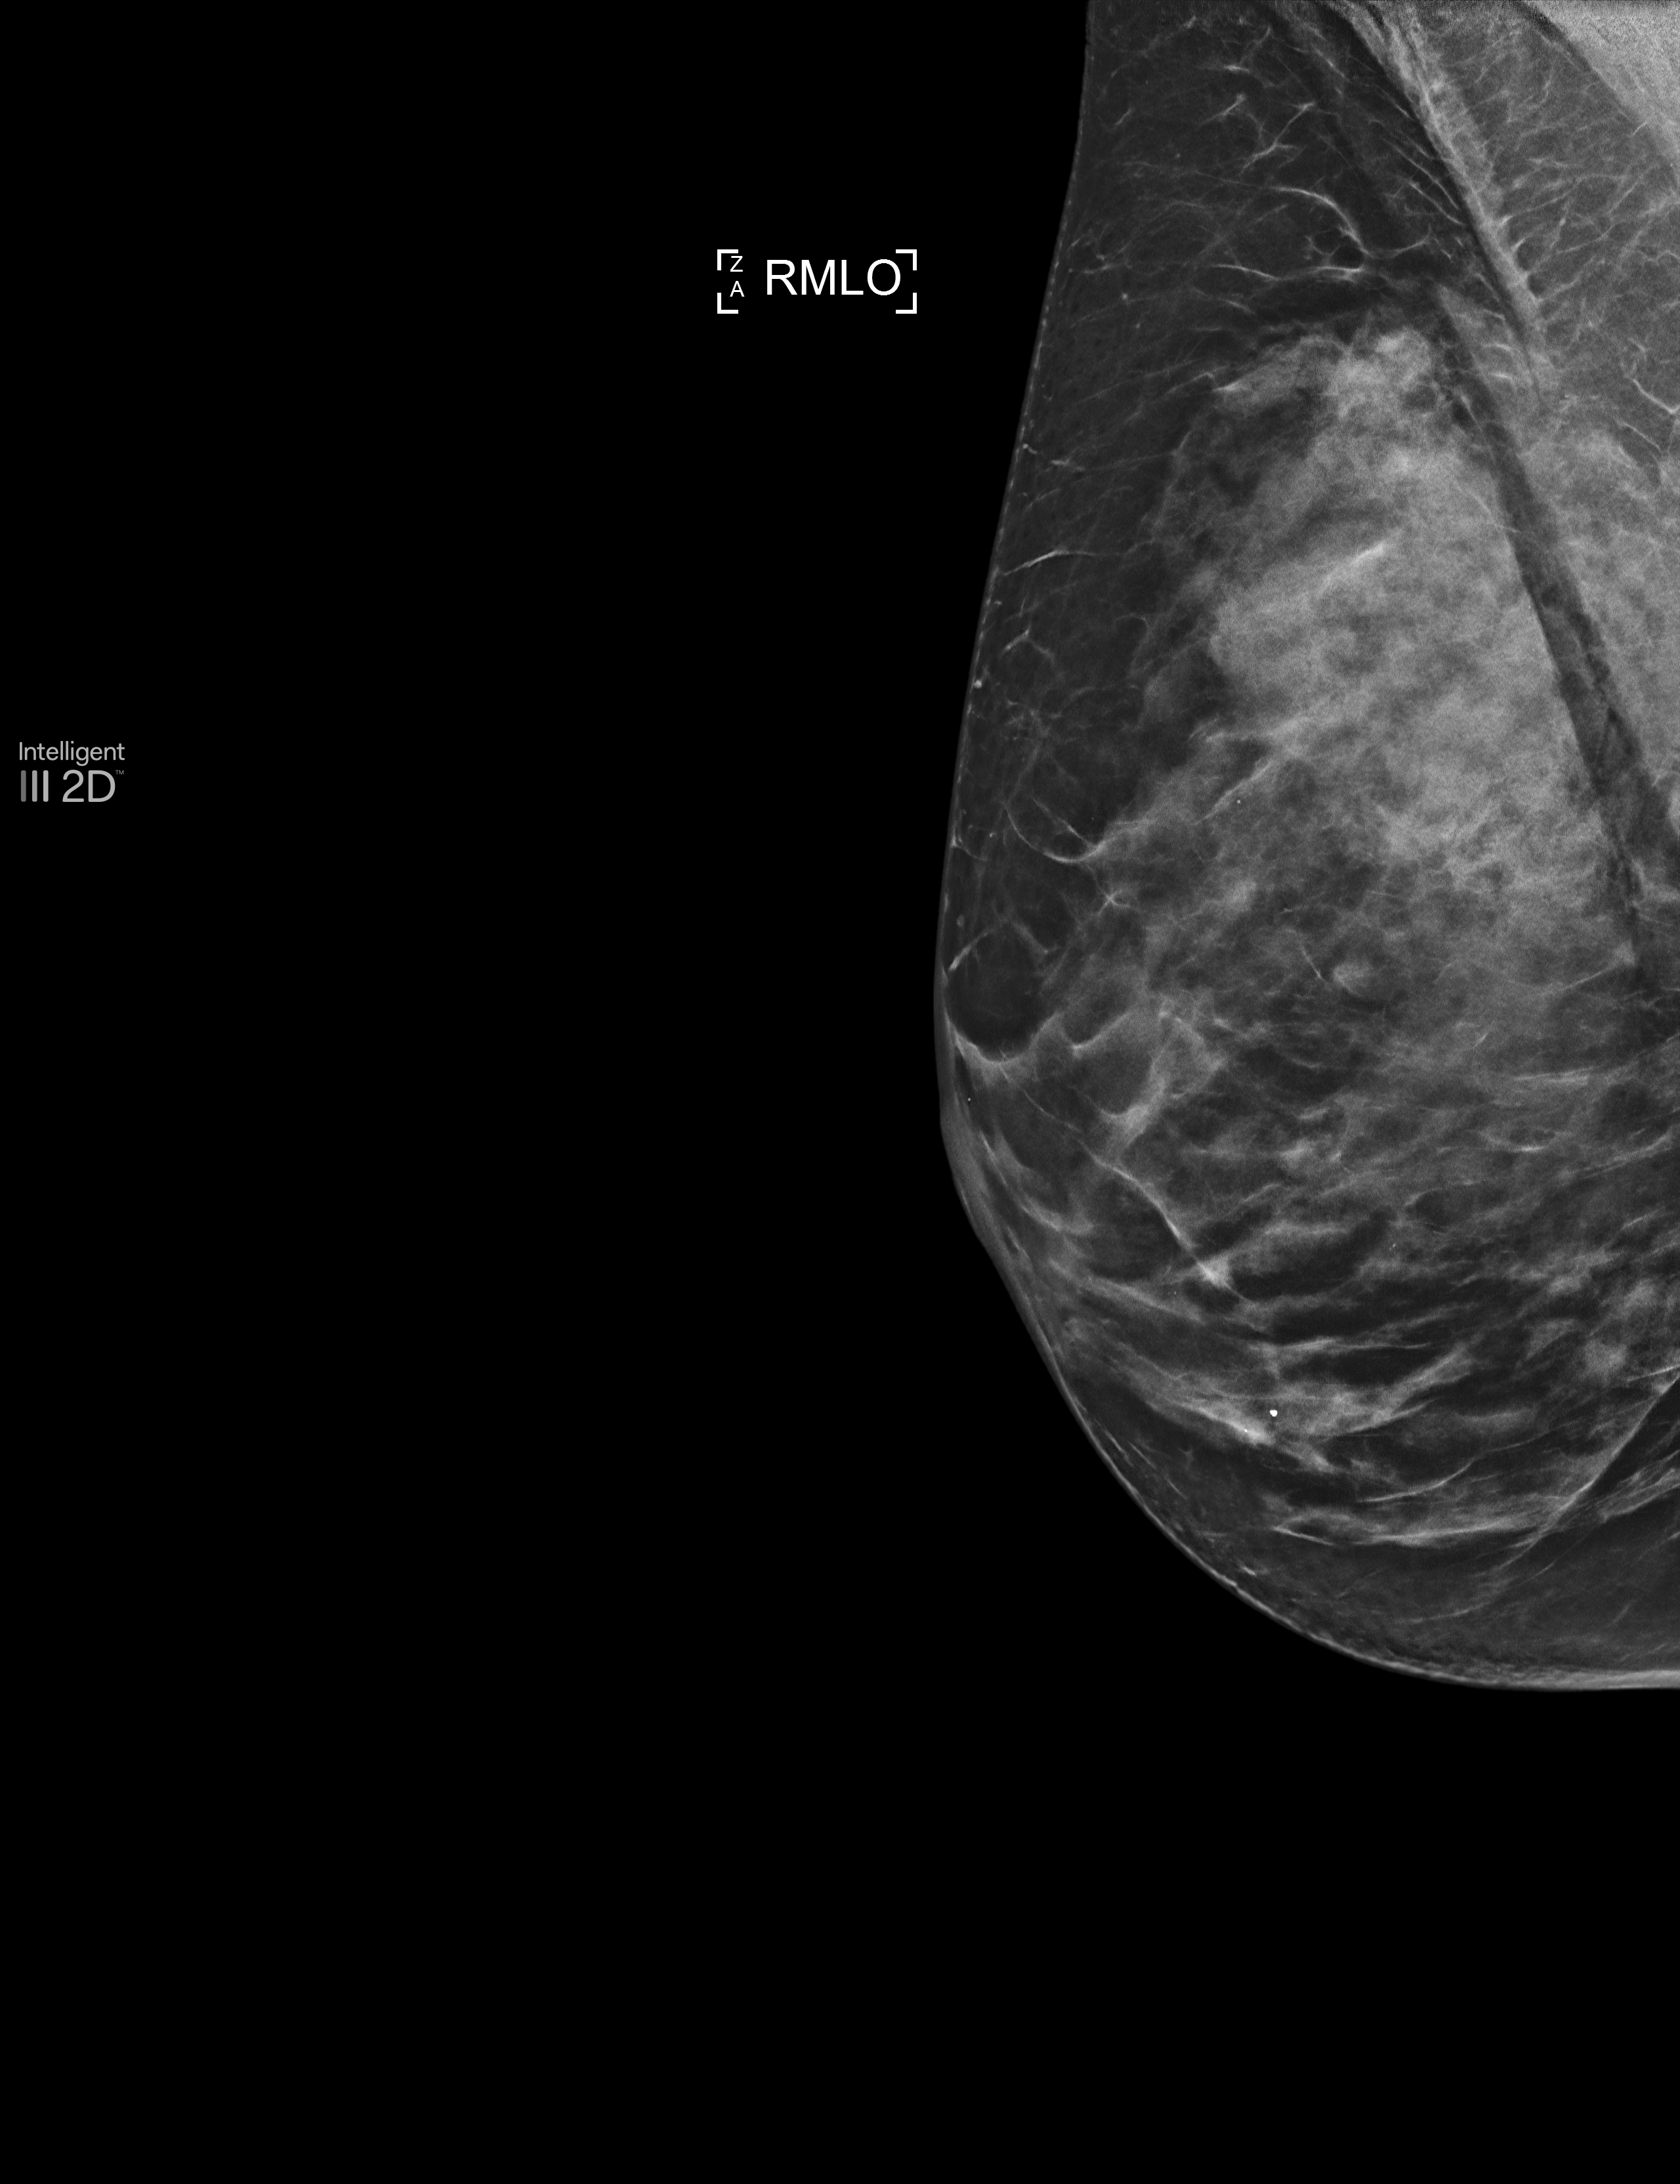
Screening examination.
Image type: synthesized 2-D view from tomosynthesis. Breast: right. Projection: medio-lateral oblique projection.